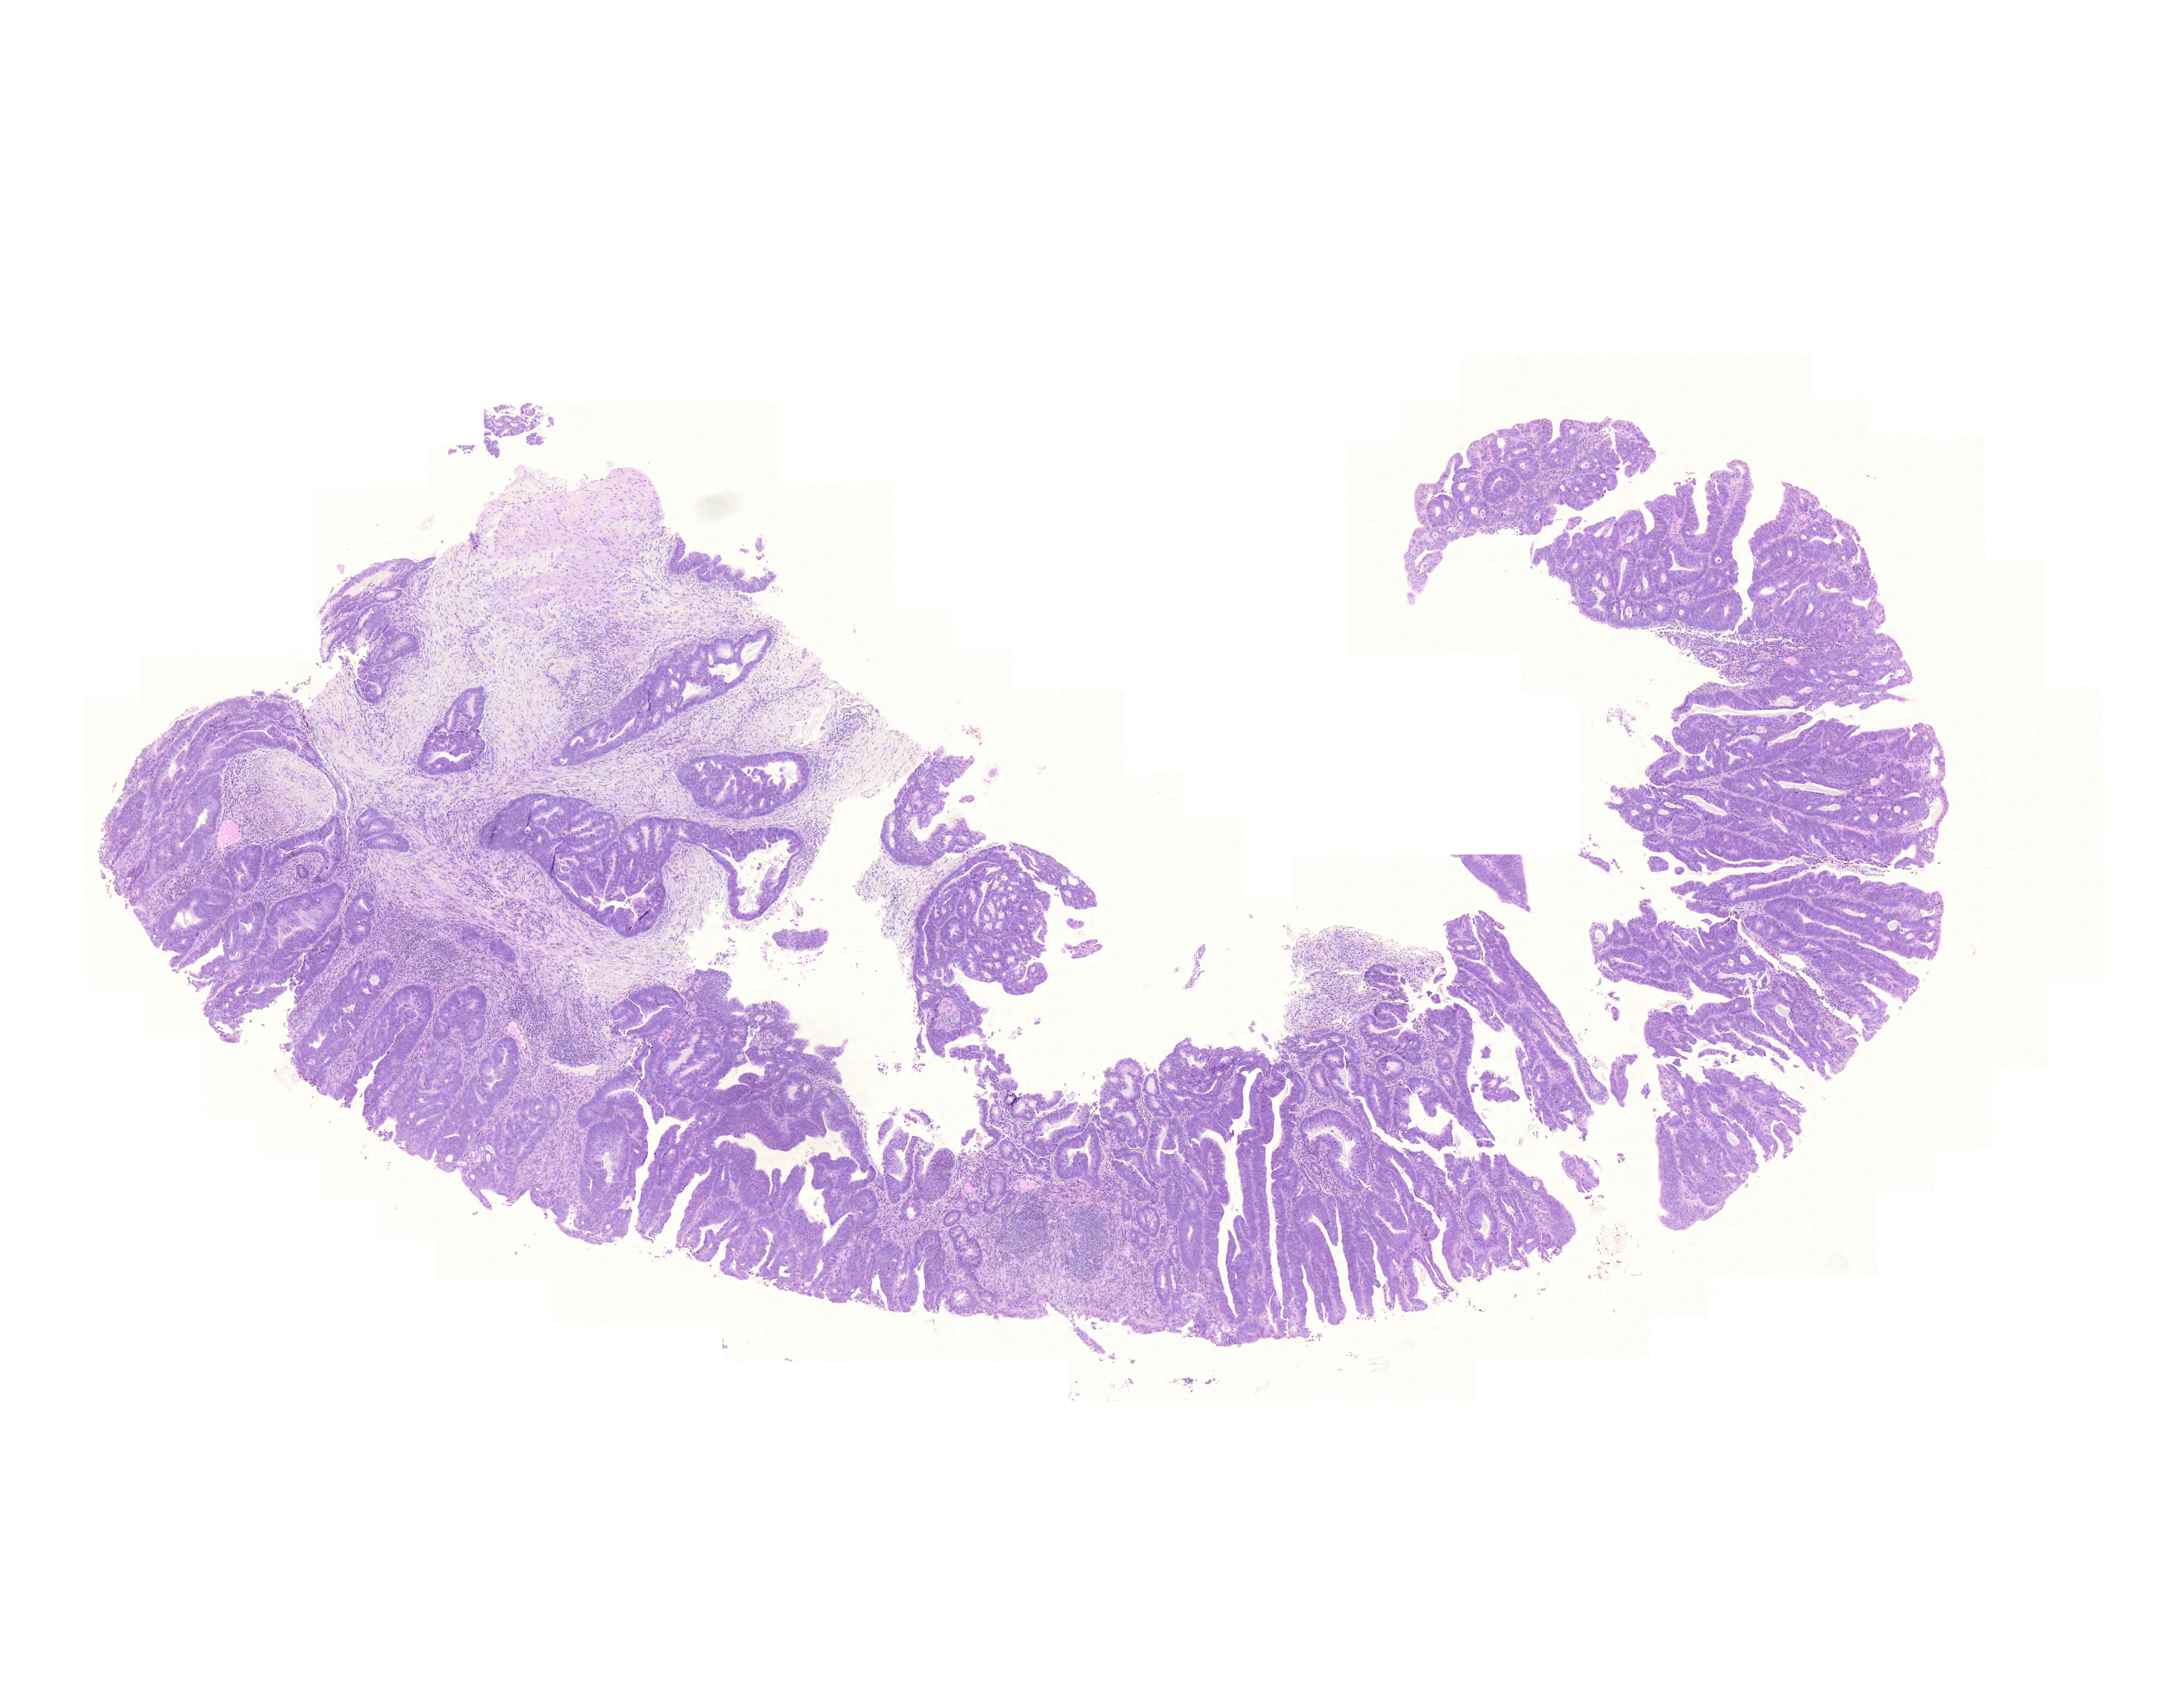
Digitized Hematoxylin and eosin (H&E) stained tissue section (whole slide) — shown as a low-resolution overview of the whole scanned area (about 10.8 x 8.5 mm, slide scanned at 20x); formalin-fixed paraffin-embedded (FFPE) diagnostic section; sample: primary tumour, colon. Female patient; age at initial diagnosis 53 years.
Lymph nodes positive (case pathology): 0 of 41 examined. Pathologic diagnosis: Adenocarcinoma, NOS. AJCC pathologic stage: II (5th edition).